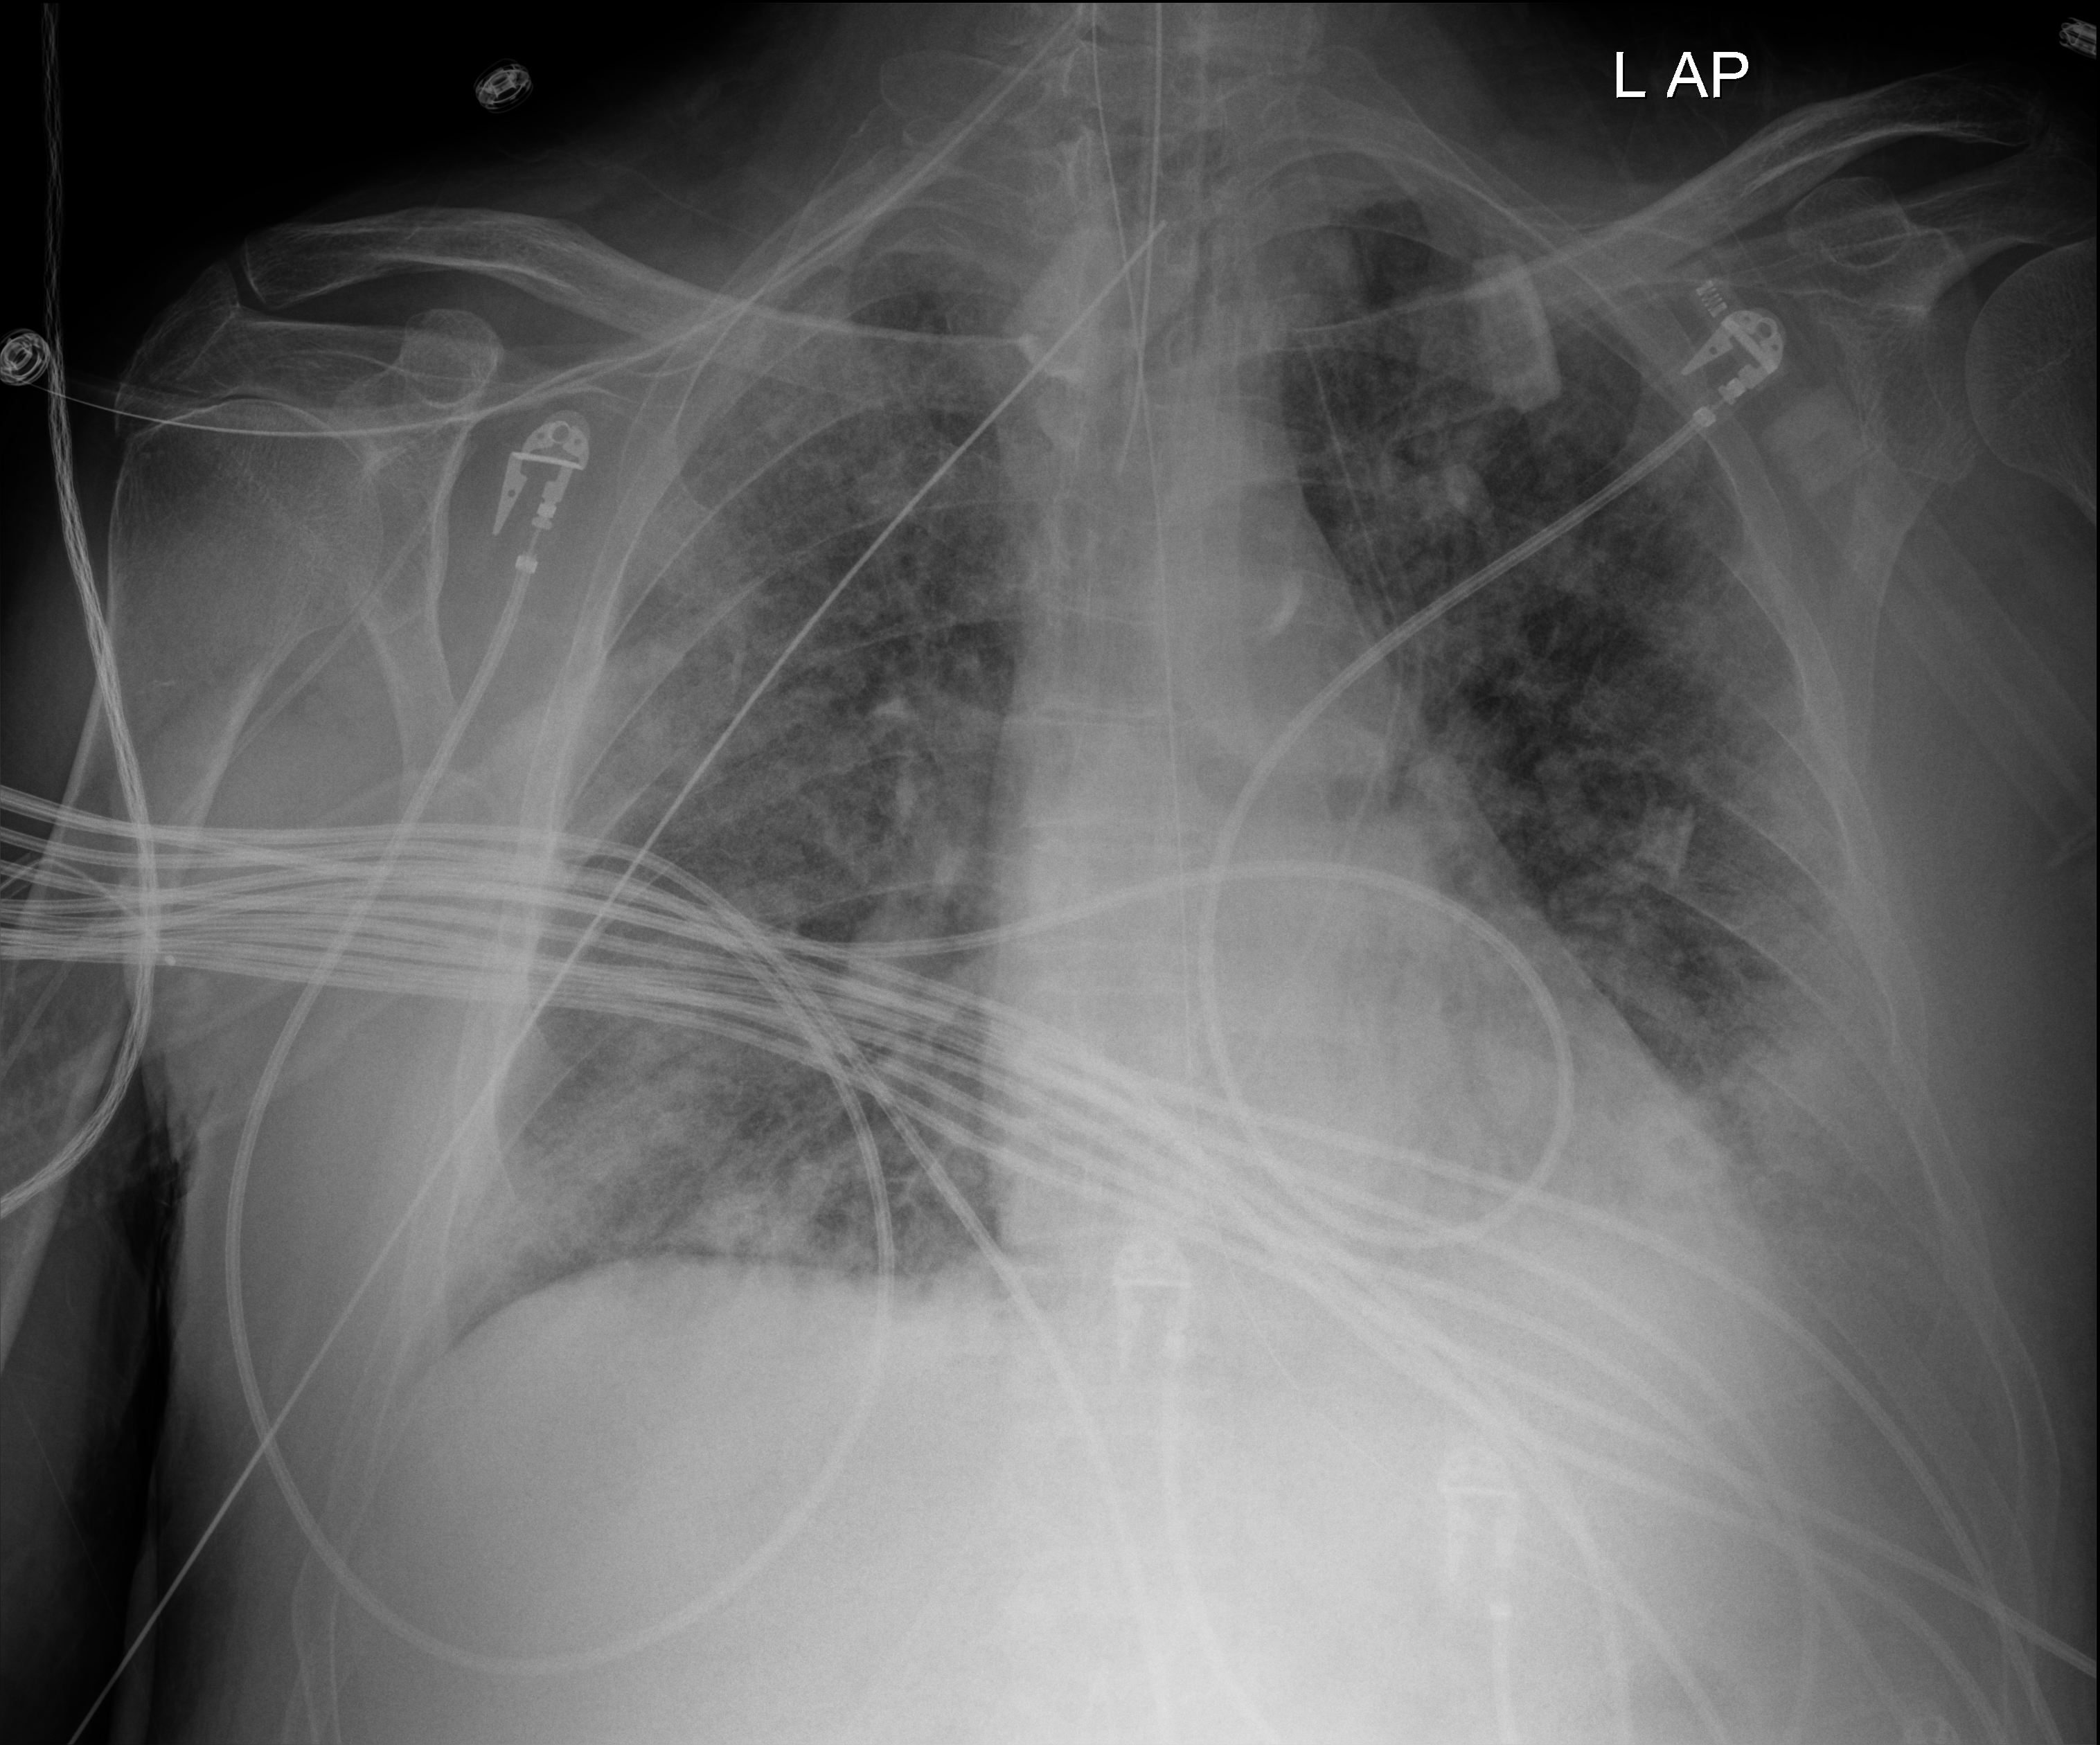
Bedside chest radiograph (digital radiography); anteroposterior (AP) projection. Male patient hospitalised with COVID-19, age 60–74 years.
Admission-level facts for this patient (not findings on this image; timing relative to this image not recorded): chronic kidney disease (admission record): no.